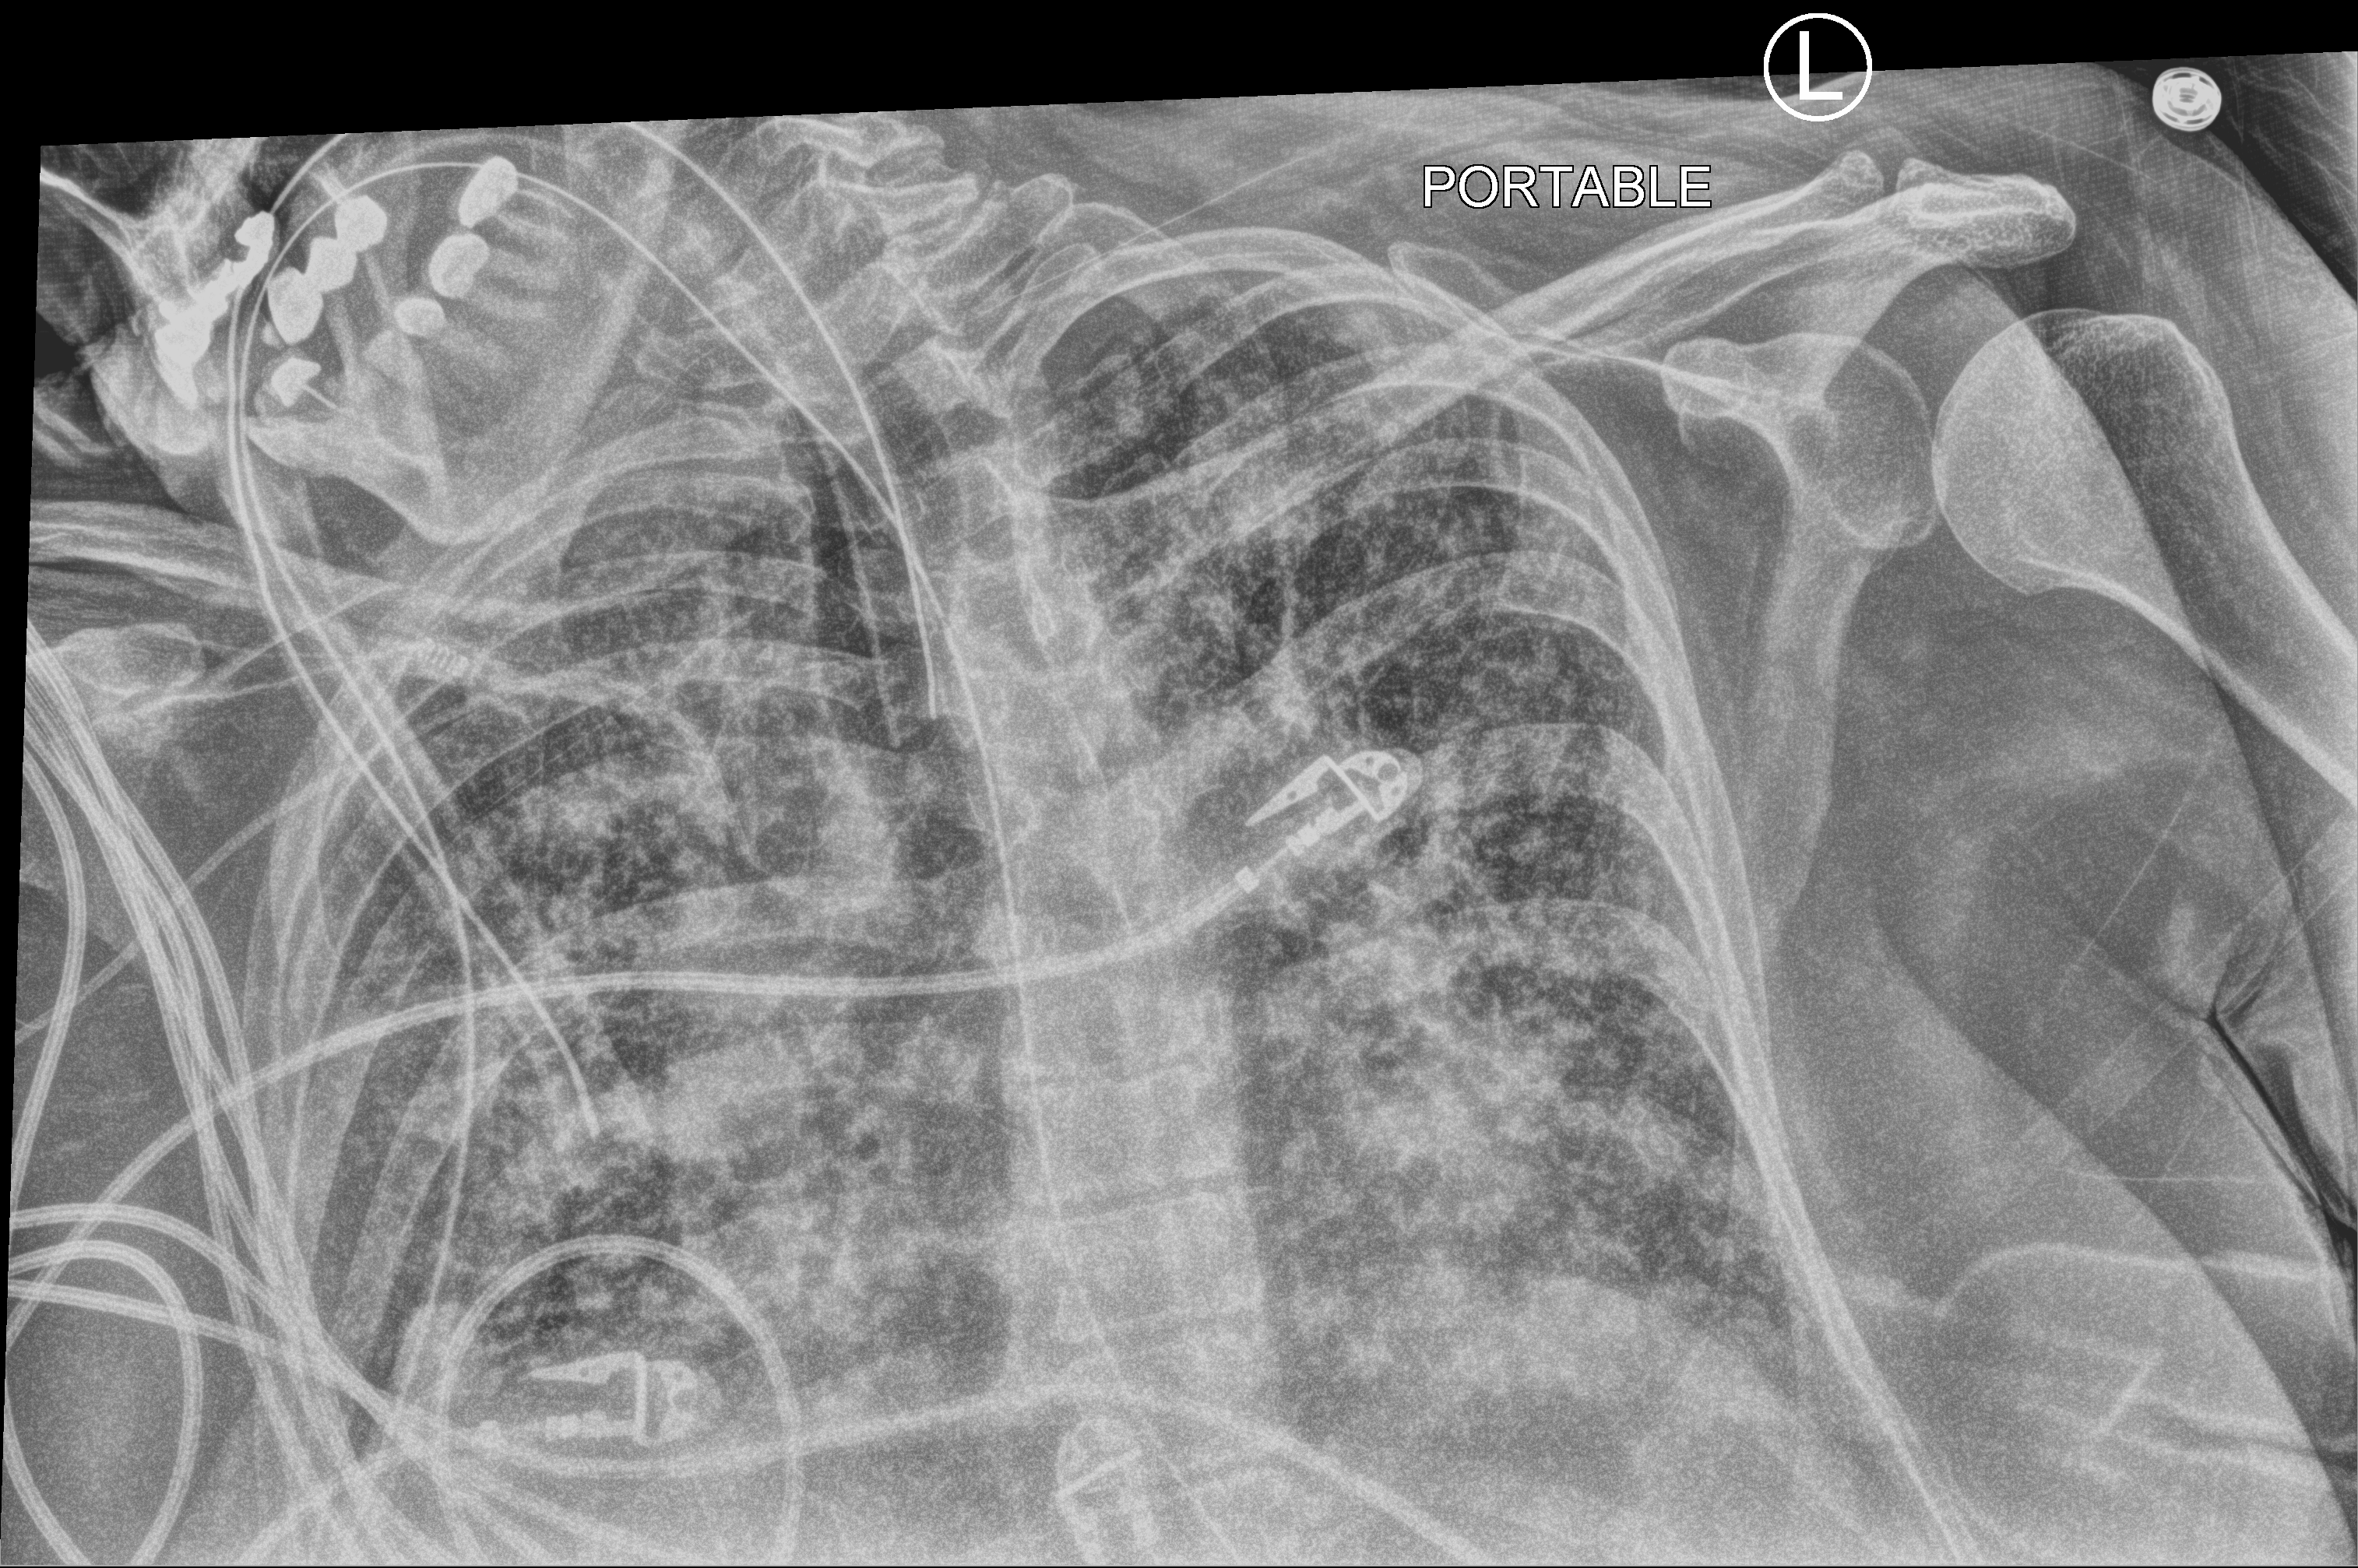
Chest X-ray (portable); anteroposterior (AP) projection. Female patient hospitalised with COVID-19, age 60–74 years.
Hospital-stay facts (about this admission, not read from this image; timing relative to this image not recorded):
- admitted to intensive care during this hospital stay: yes